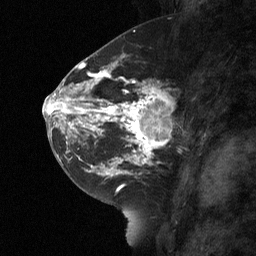
Breast MRI (dynamic contrast-enhanced), one sagittal slice. Dynamic contrast-enhanced study with each time point stored as its own series, time point 2 of 3 at this slice position (early post-contrast, ordered by acquisition time). 1.5 T. TE 4.8 ms, TR 27 ms. 256 × 256 image matrix, field of view 180 × 180 mm. Patient: female, 42 years. Case-level facts recorded for this patient, not image findings: setting: breast cancer imaged before/during neoadjuvant chemotherapy; receptor status: triple-negative.
Annotated regions visible in this slice (semi-automatic segmentation, software-assisted and operator-edited):
- analysis volume of interest (the breast-tissue region the enhancement analysis was run in; not a lesion): bounding box <115,85,189,160> (left, top, right, bottom; pixels)
- tumour enhancement mask (voxels above the 90 % enhancement threshold inside the analysis volume of interest): <115,85,172,160>